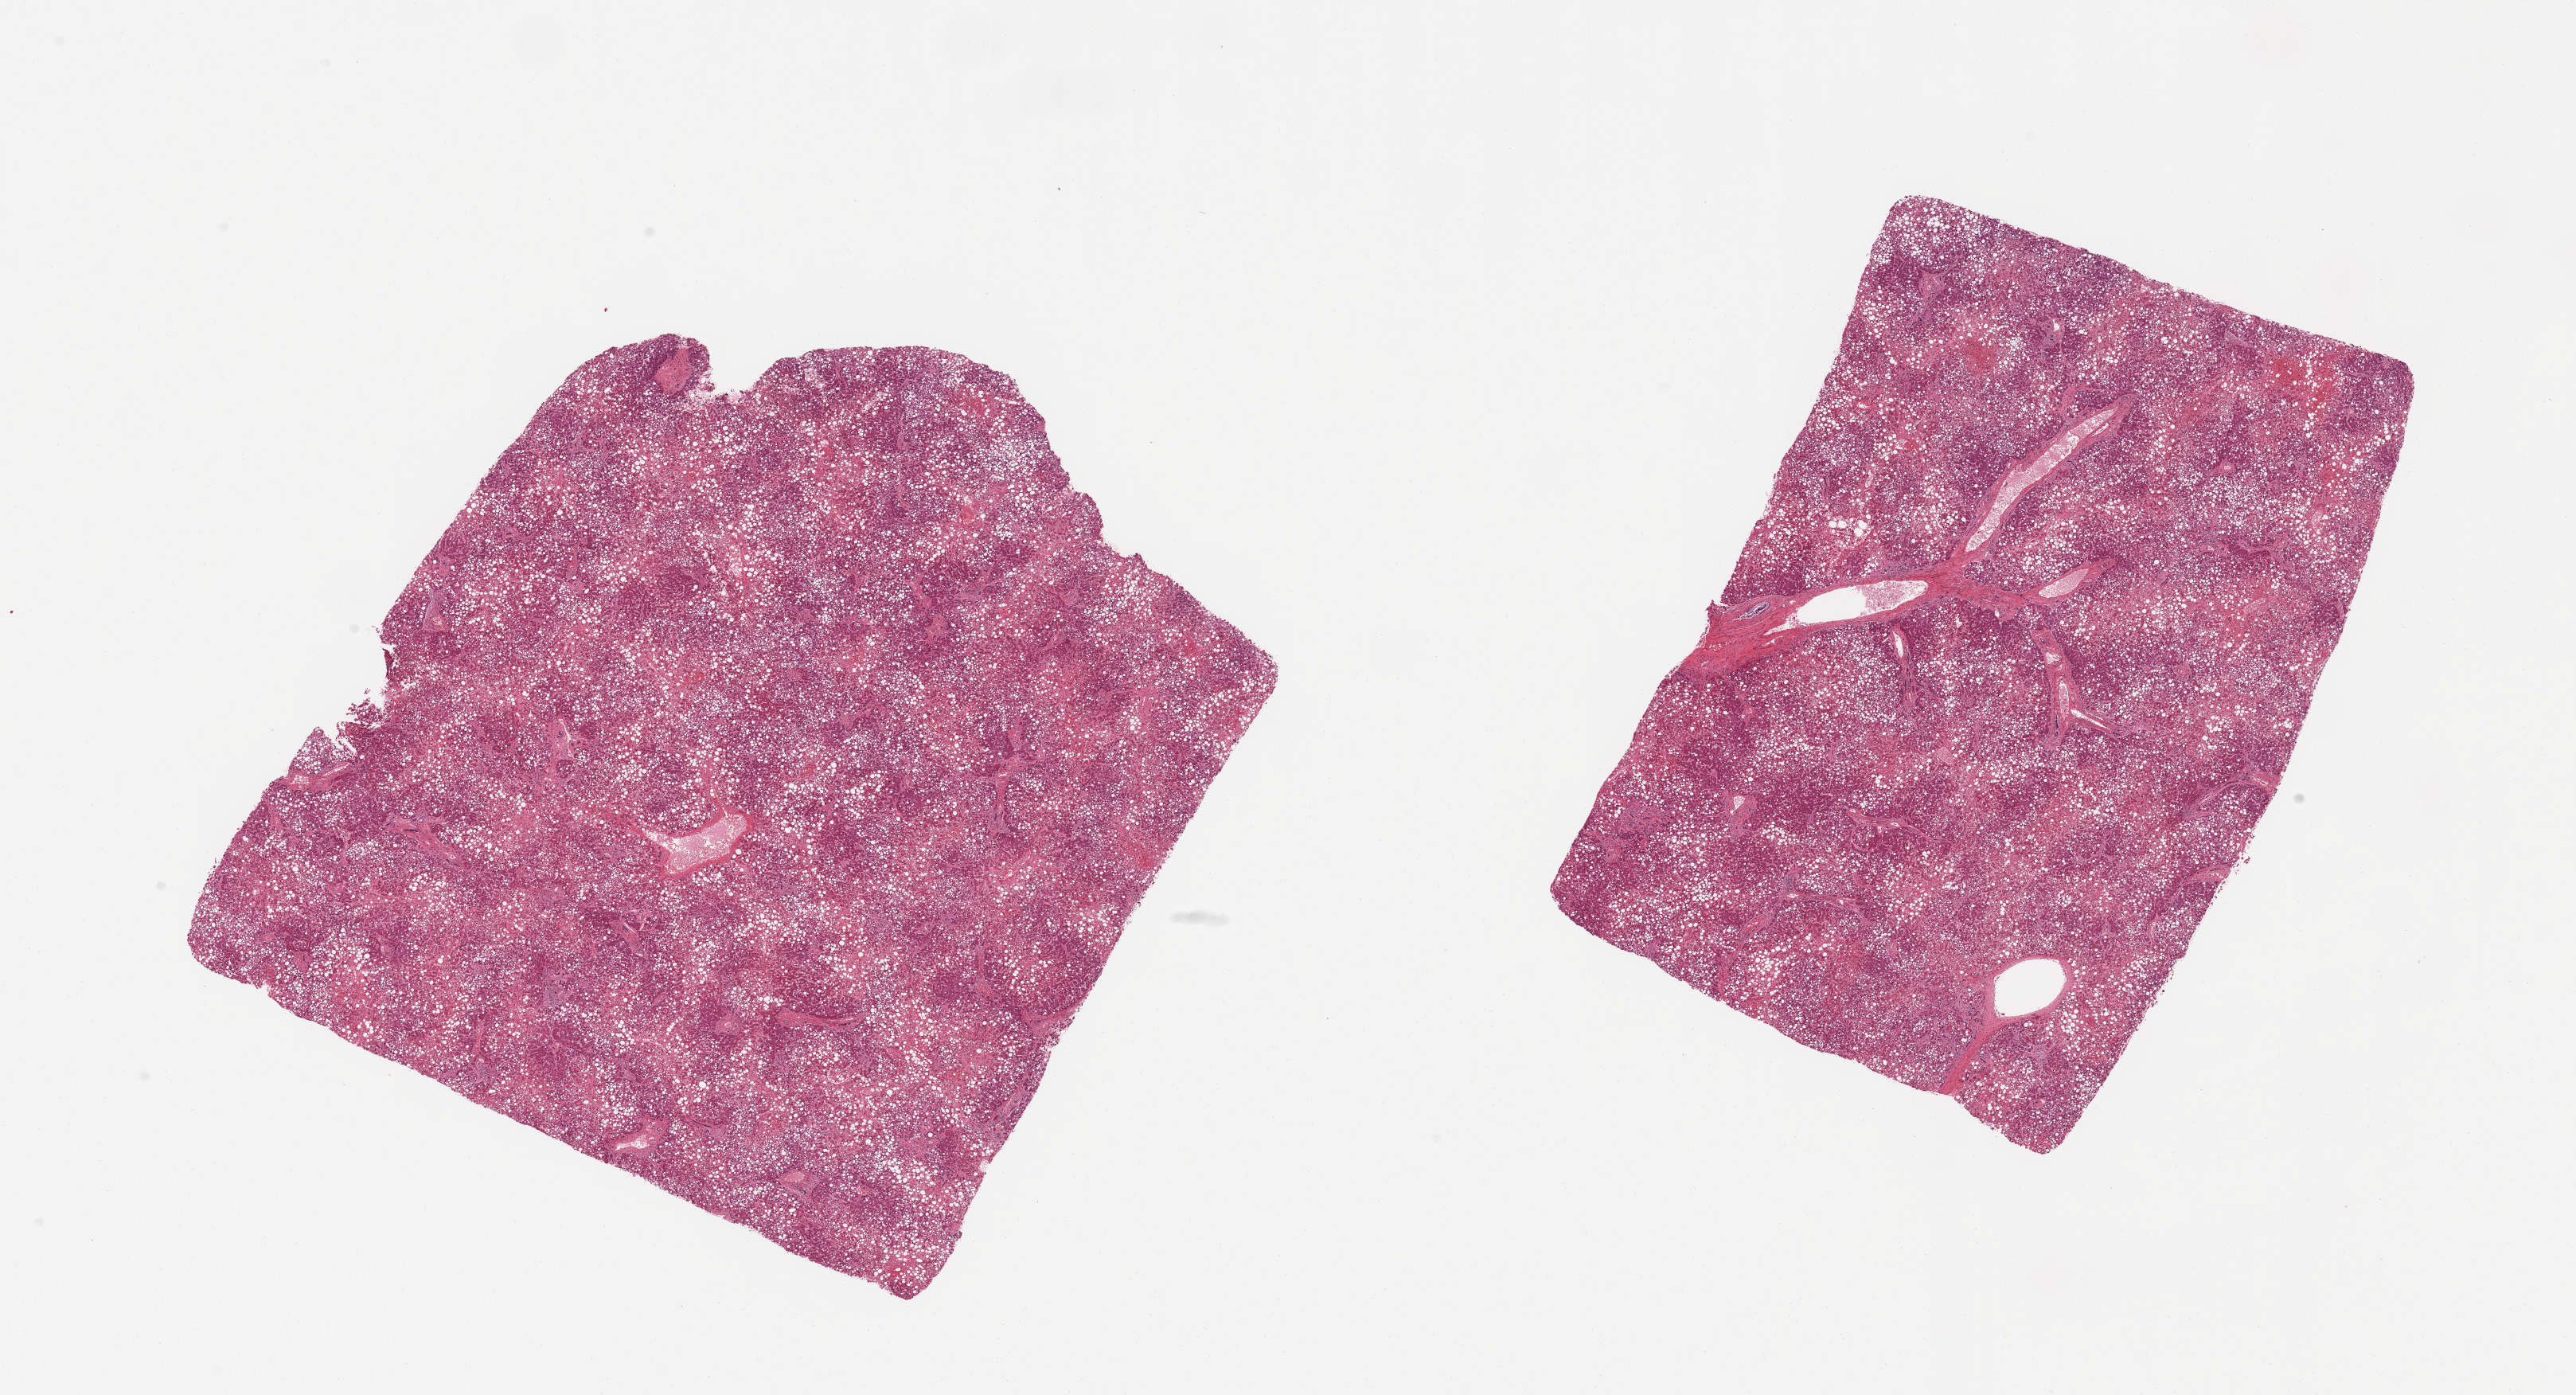
Hematoxylin and eosin (H&E) whole-slide image — shown as a low-resolution overview of the whole scanned area (about 25.6 x 13.9 mm, slide scanned at 20x). PAXgene-fixed paraffin-embedded (PFPE) section. Target tissue: liver. Donor tissue sample.
Review note (as recorded): 2 pieces; severe macrovesicular steatosis, centrilobular congestion, fibrosis.